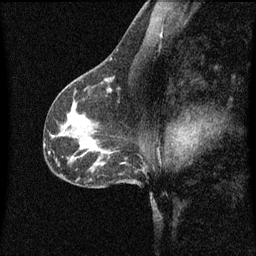
Breast MRI (dynamic contrast-enhanced), one sagittal slice. Position 36 of 60 along the scan axis. Dynamic contrast-enhanced series, image 2 of 3 at this slice position (ordered by acquisition). 1.5 T. TE 4.2 ms, TR 8.4 ms. 2 mm slice thickness. 256 × 256 image matrix, field of view 200 × 200 mm. Female patient, age 41 years.
Structures marked on this image (semi-automatically segmented with operator editing):
- analysis volume of interest (the breast-tissue region the enhancement analysis was run in; not a lesion): bounding box [x1, y1, x2, y2] px = [94, 72, 119, 97]
- tumour enhancement mask (voxels above the 70 % enhancement threshold inside the analysis volume of interest): [102, 78, 119, 89]